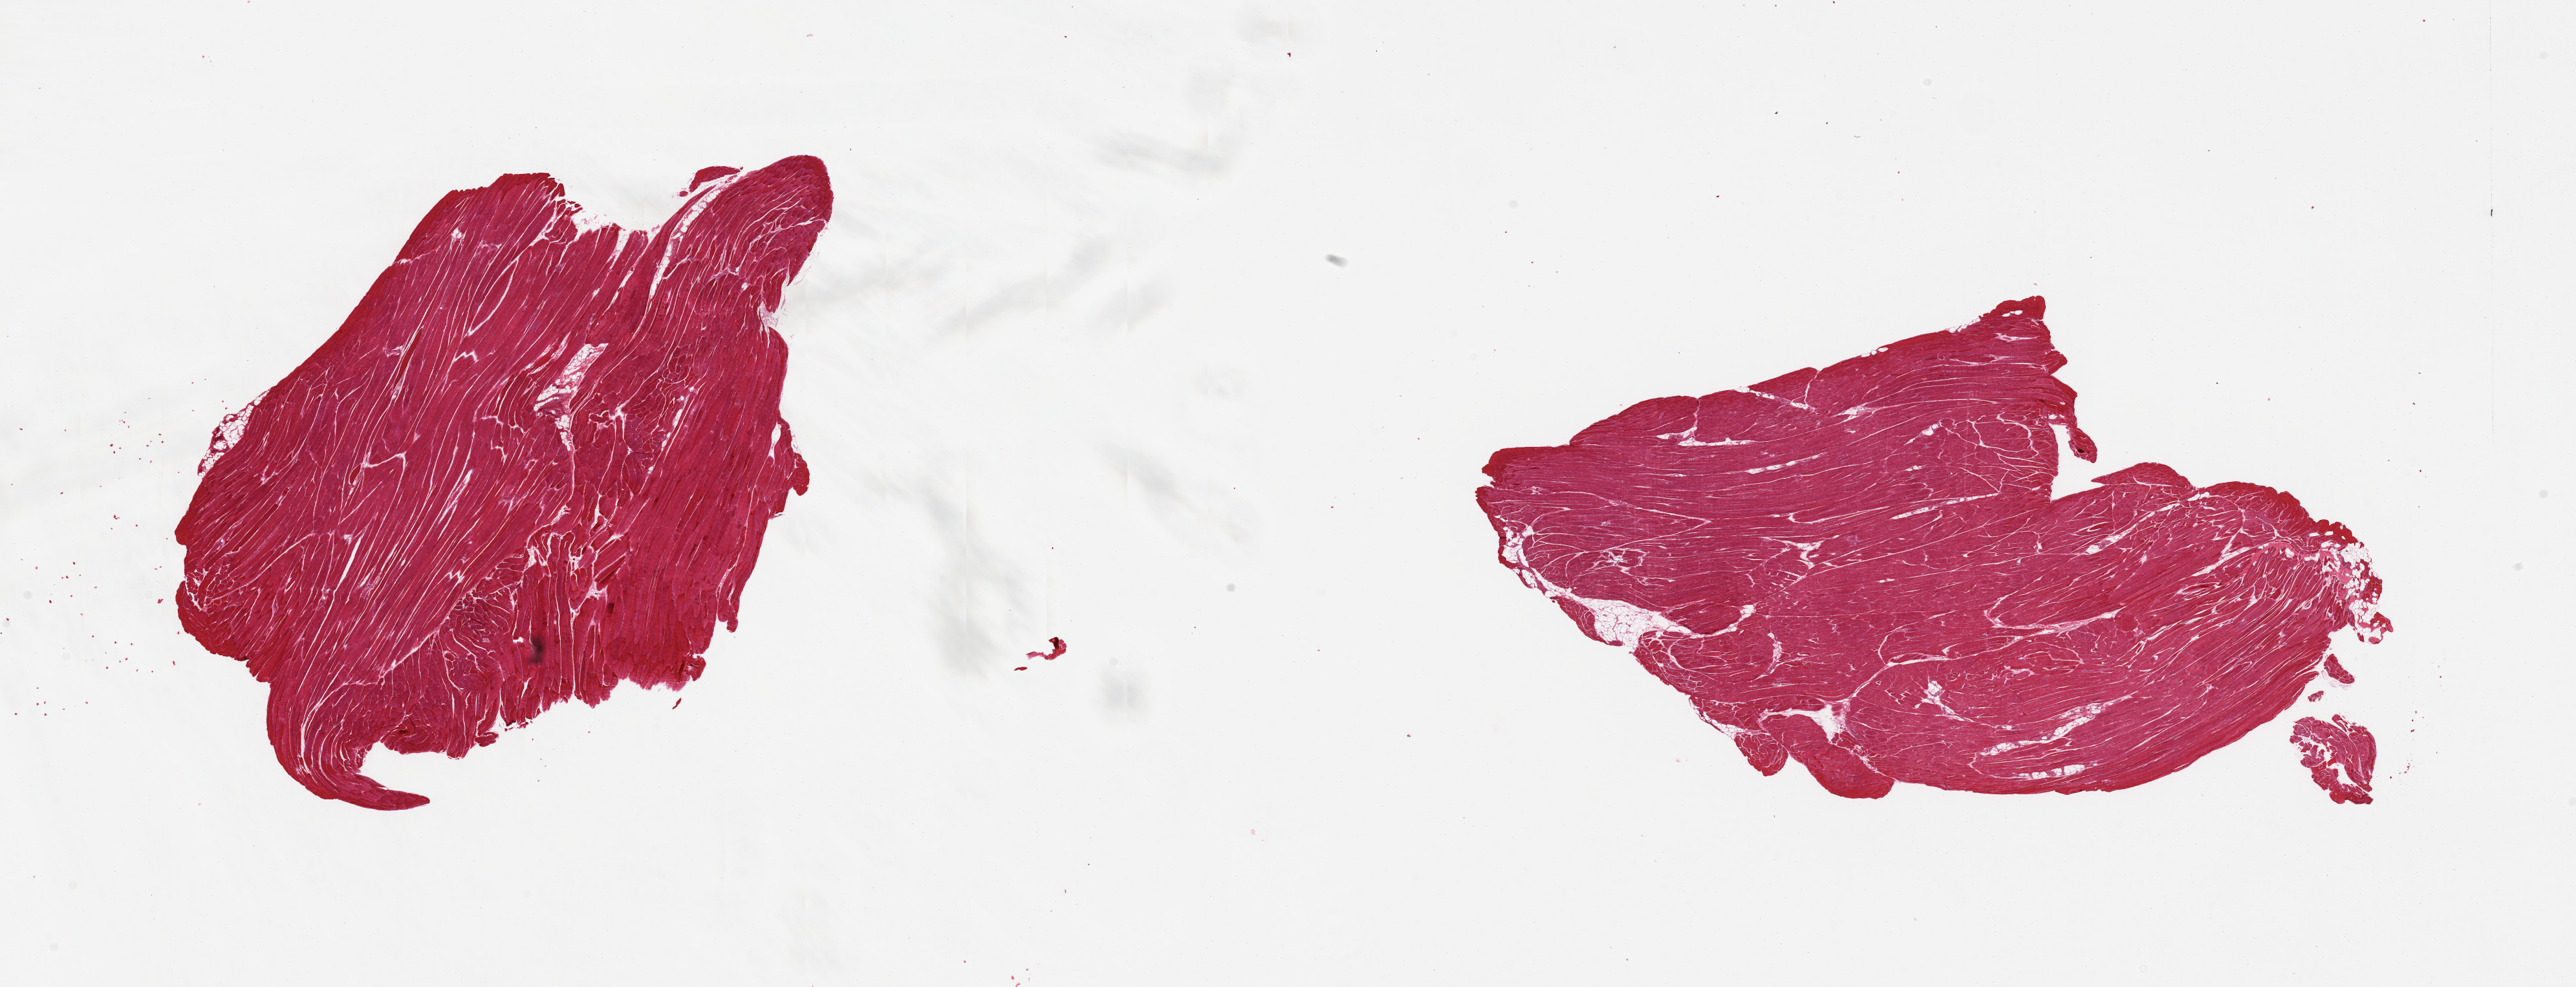
Digitized haematoxylin and eosin-stained section — whole scanned area (about 31.5 x 12.1 mm) shown as a low-resolution overview. PAXgene-fixed, paraffin-embedded tissue. Target tissue: skeletal muscle. Donor tissue sample. Female donor.
• pathologist's review note for this sample: 2 pieces